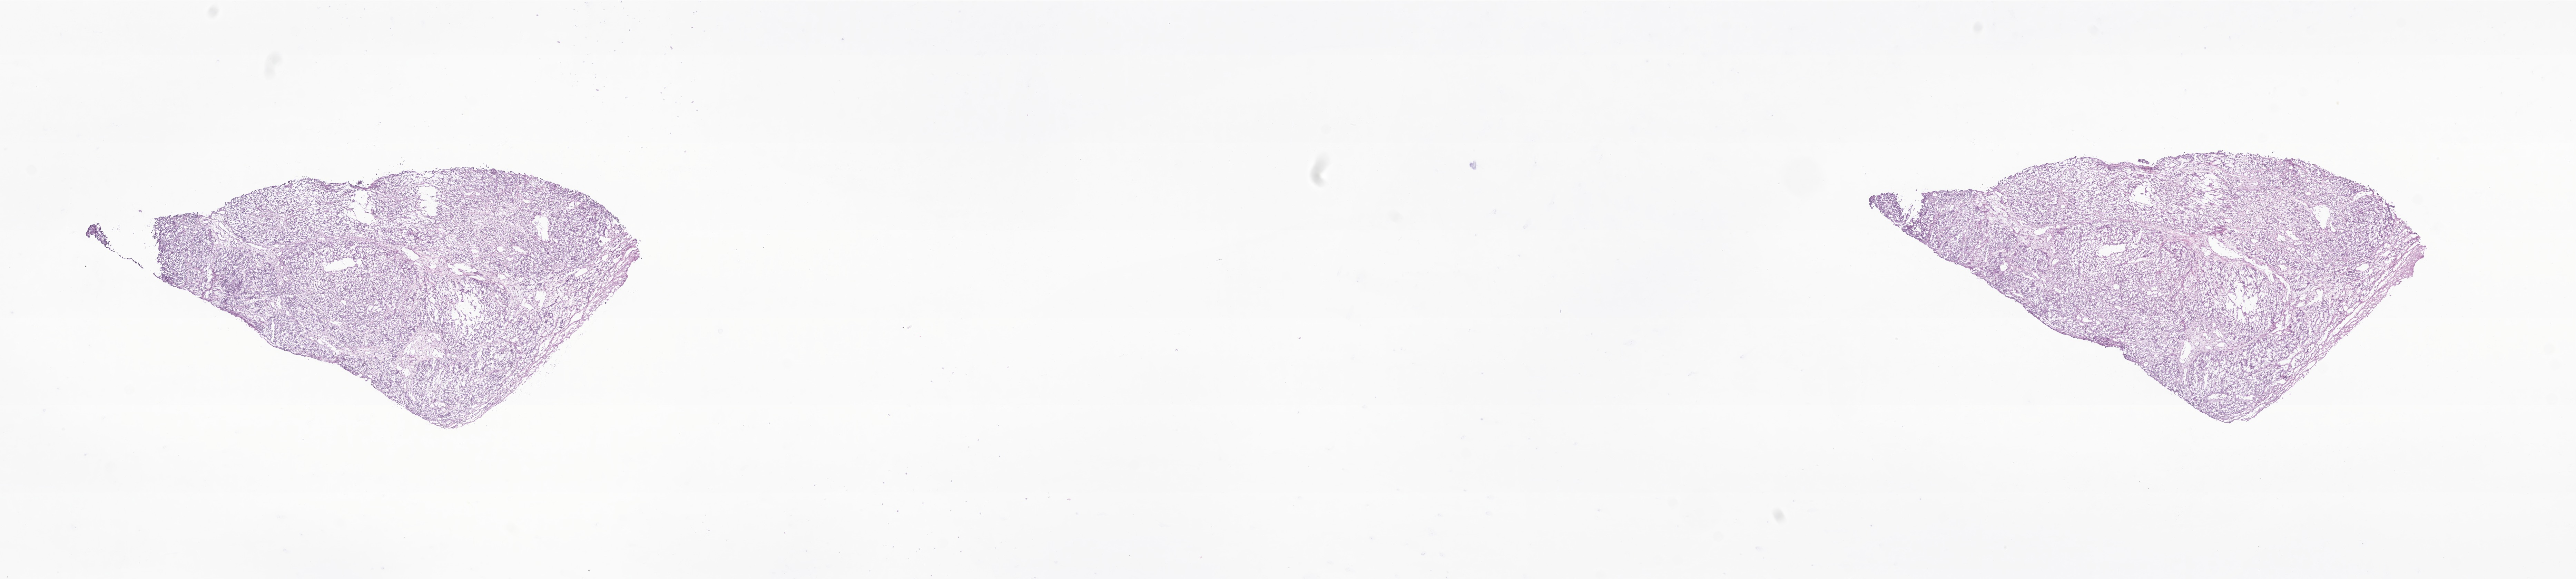
Whole-slide image, haematoxylin and eosin stain of tumor tissue from the brain — a low-resolution overview of the entire scanned area, about 31.5 x 7.1 mm. Cryosection (OCT / tissue freezing medium). Male patient, age 87 months.
Diagnosis (ICD-O-3 morphology term): Glioma, malignant.